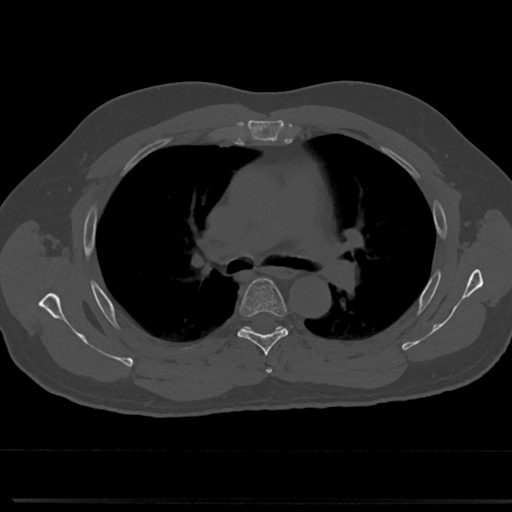
CT including the spine, one axial slice; slice 494 of 817 in the series (ordered by position); reconstruction kernel Br40s/3; 120 kVp; bone window (W 1800 / L 400 HU); 0.5 mm slice thickness; 512 × 512 image matrix, field of view 355 × 355 mm. Patient: male, 61 years. Case-level facts recorded for this patient, not image findings: primary cancer: prostate.
Annotated regions visible in this slice (semi-automatic segmentation, software-assisted and operator-edited):
- T4 vertebra: bounding box (x1, y1, x2, y2) in pixels: (264, 358, 273, 374)
- T5 vertebra: (218, 277, 305, 349)